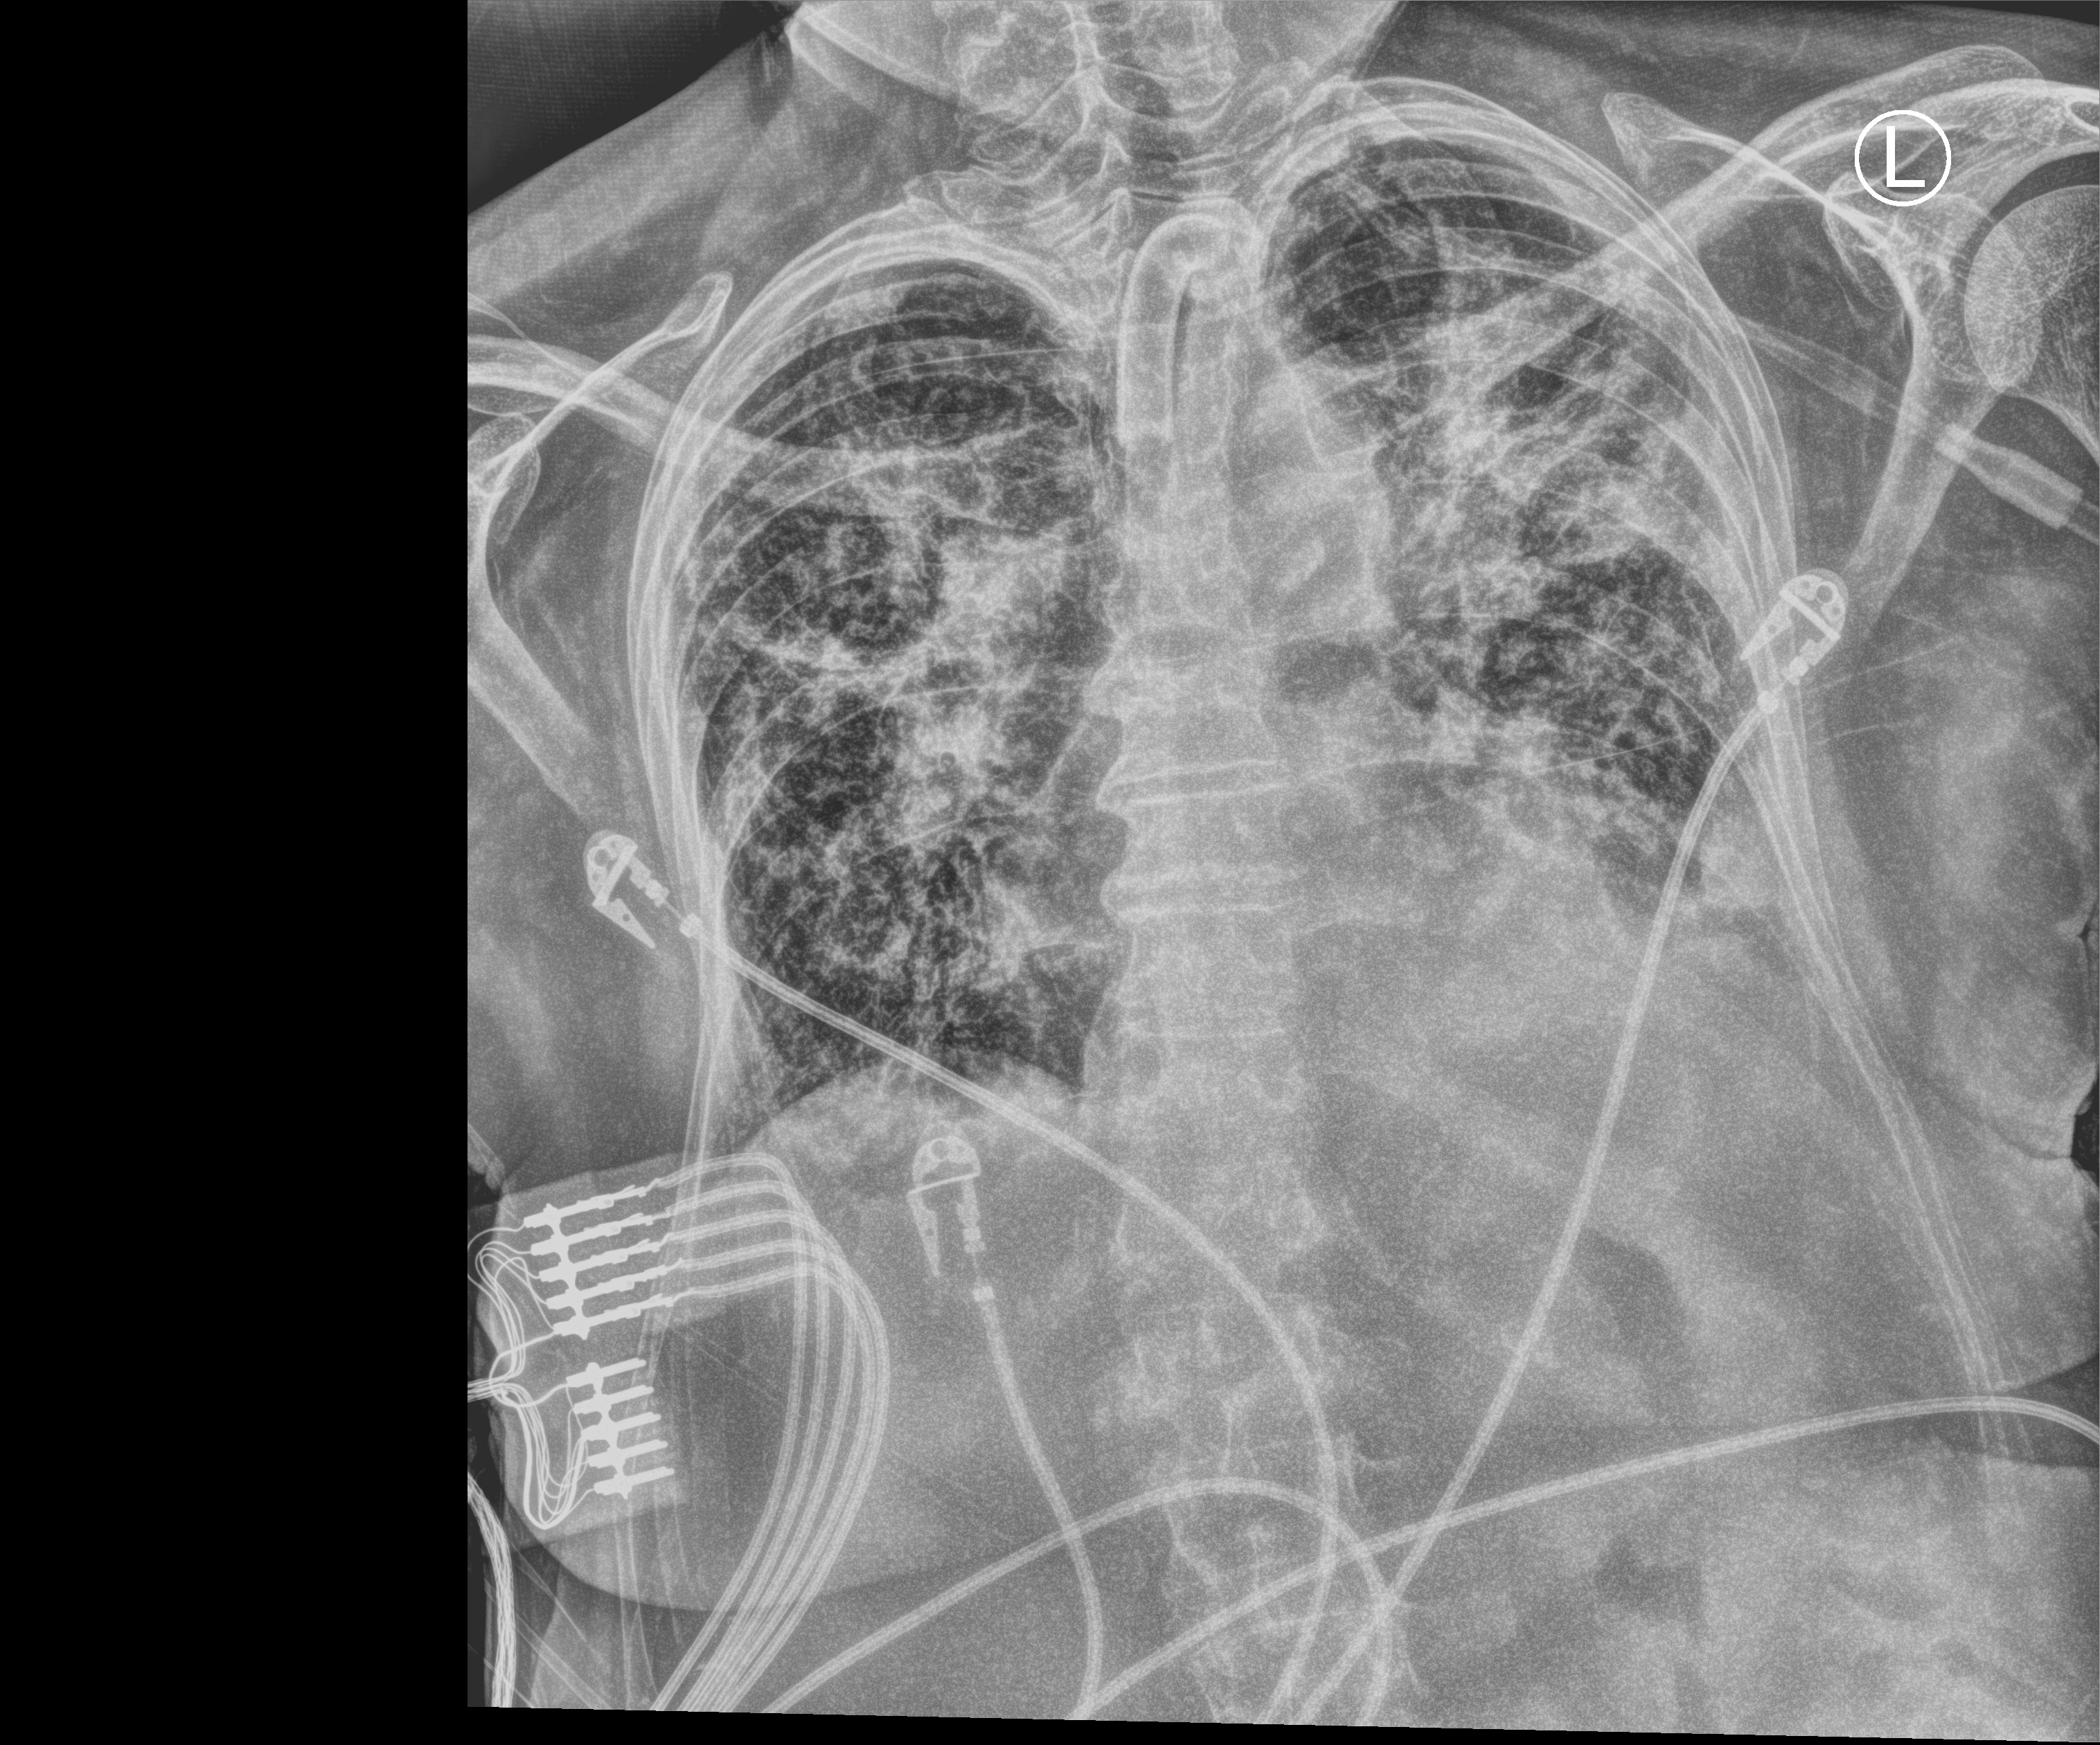
Chest X-ray (portable); anteroposterior (AP) projection. Patient hospitalised with COVID-19; female, aged 75–90 years.
From the hospital-stay record, not from the radiograph (when in the stay this image was taken is not recorded):
- COPD (admission record): no